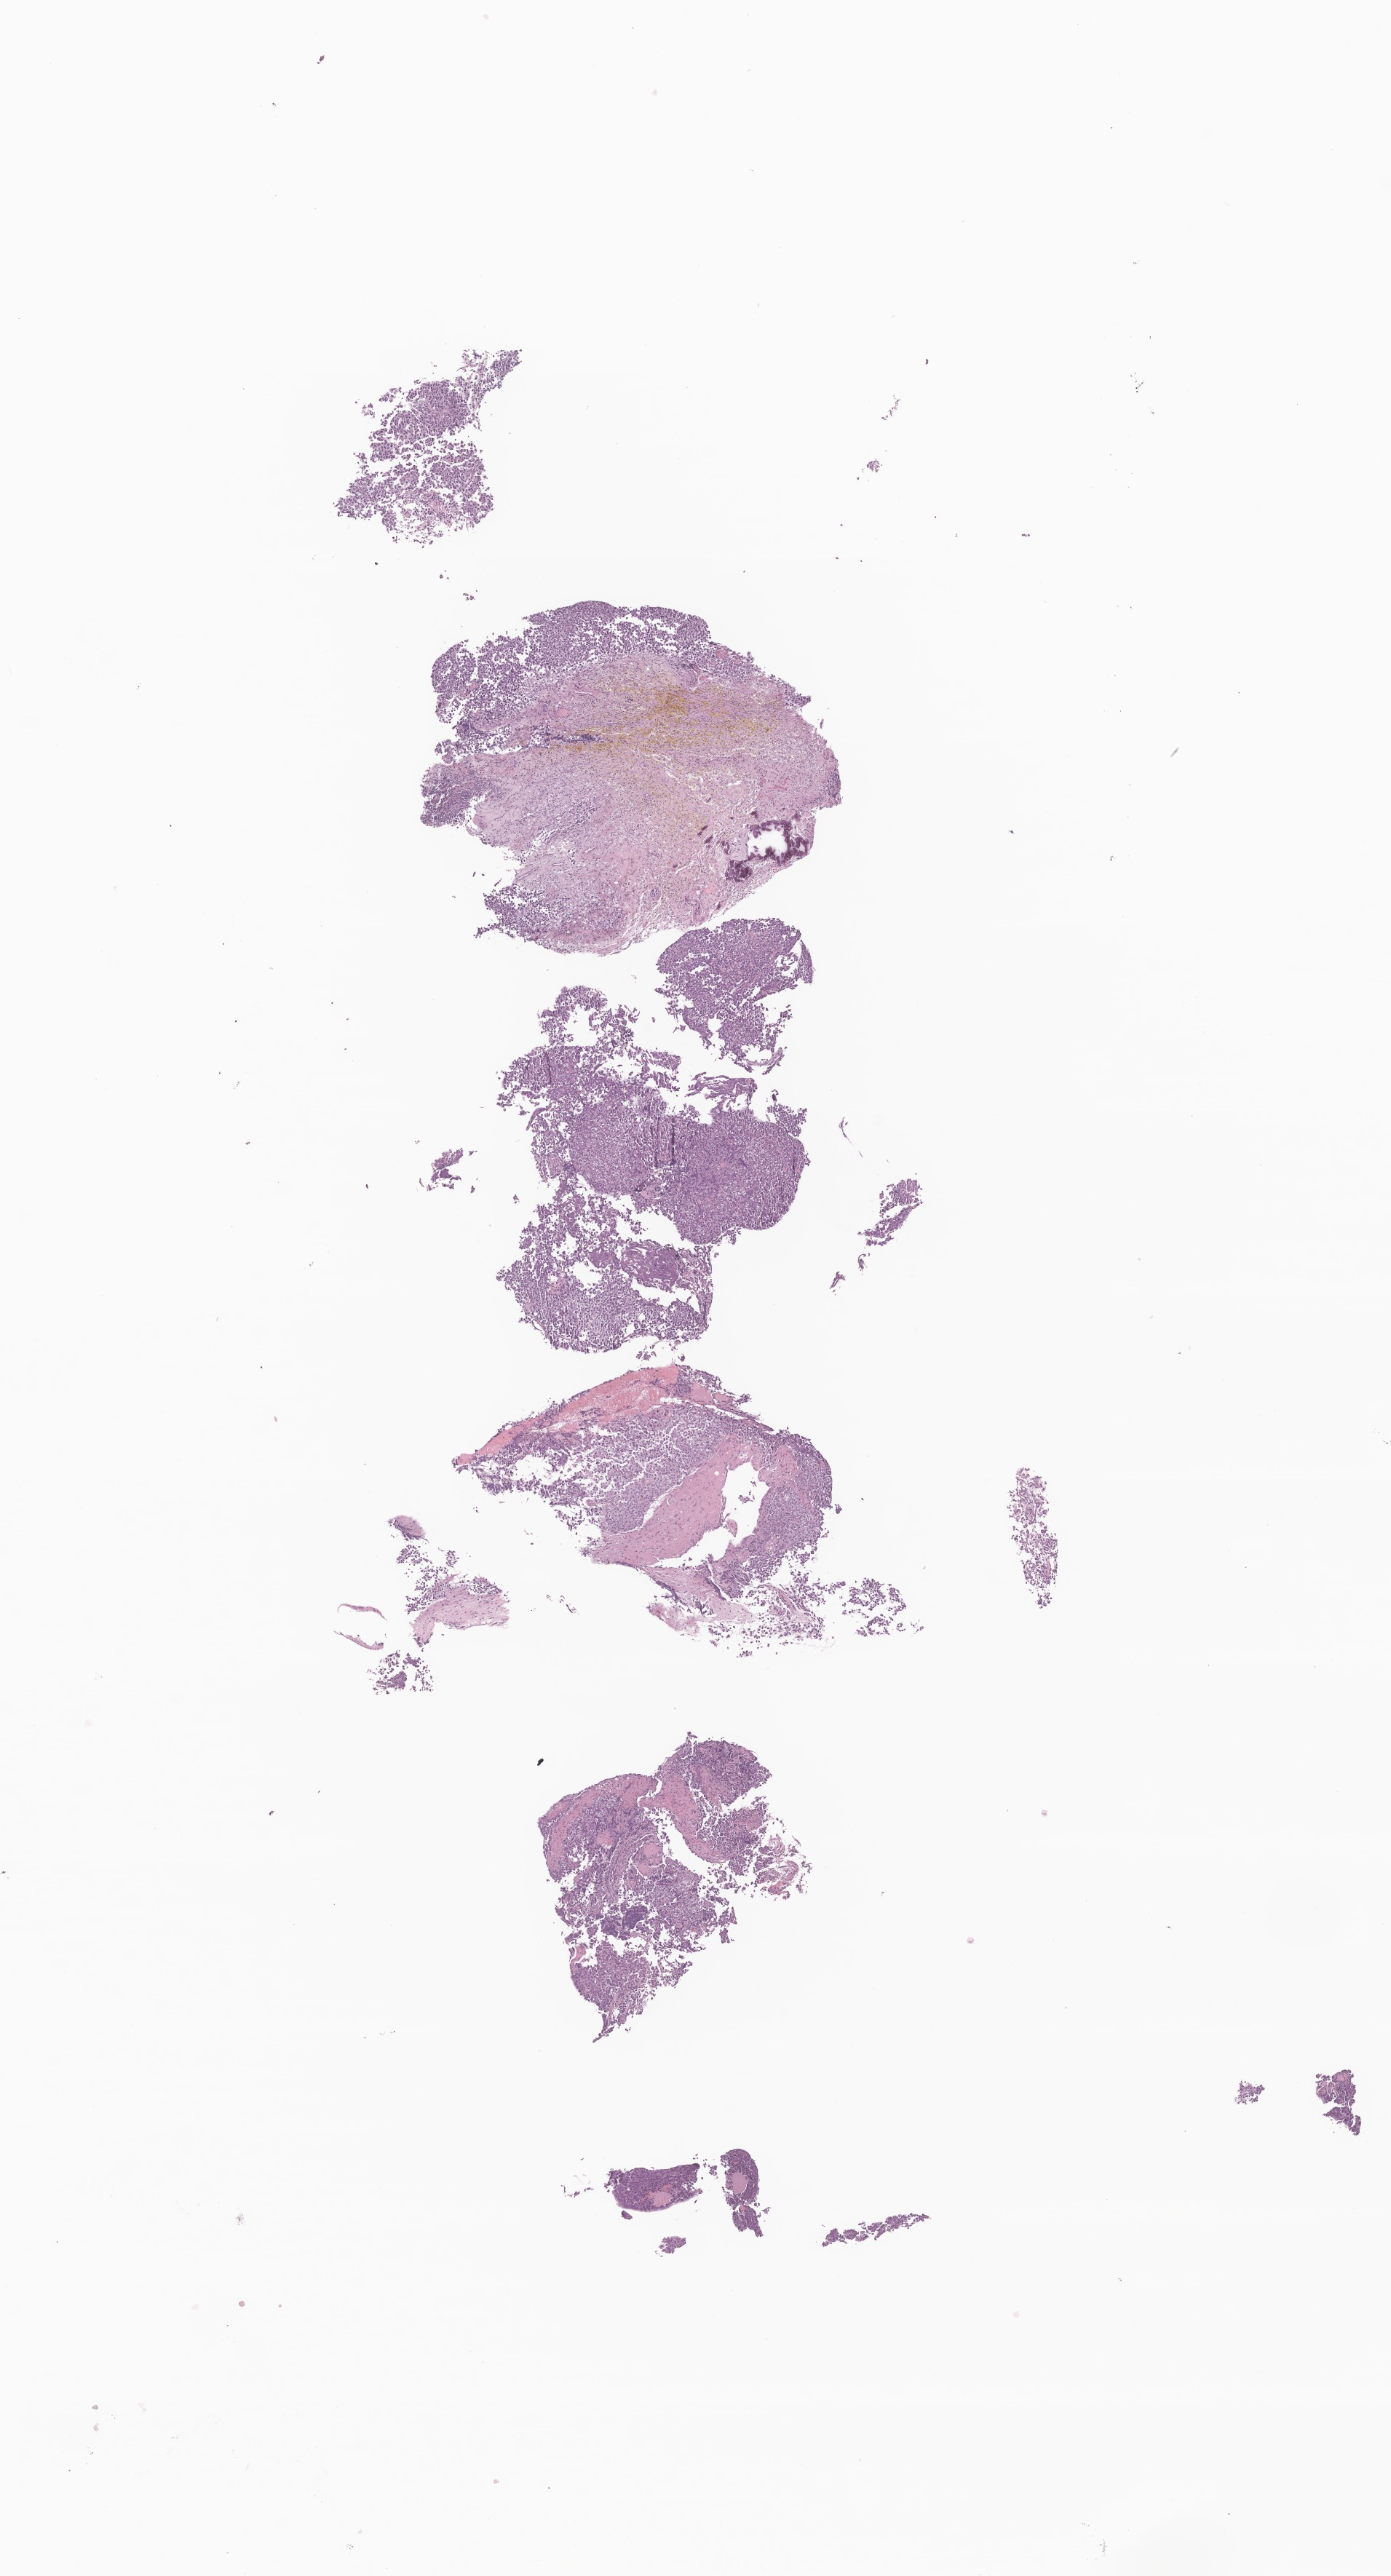
Digitized haematoxylin and eosin-stained section of tumor tissue from the brain — whole scanned area (about 8.1 x 14.9 mm) shown as a low-resolution overview; formalin-fixed paraffin-embedded section. Male patient, age 134 months.
Recorded diagnosis: Neoplasm, uncertain whether benign or malignant.